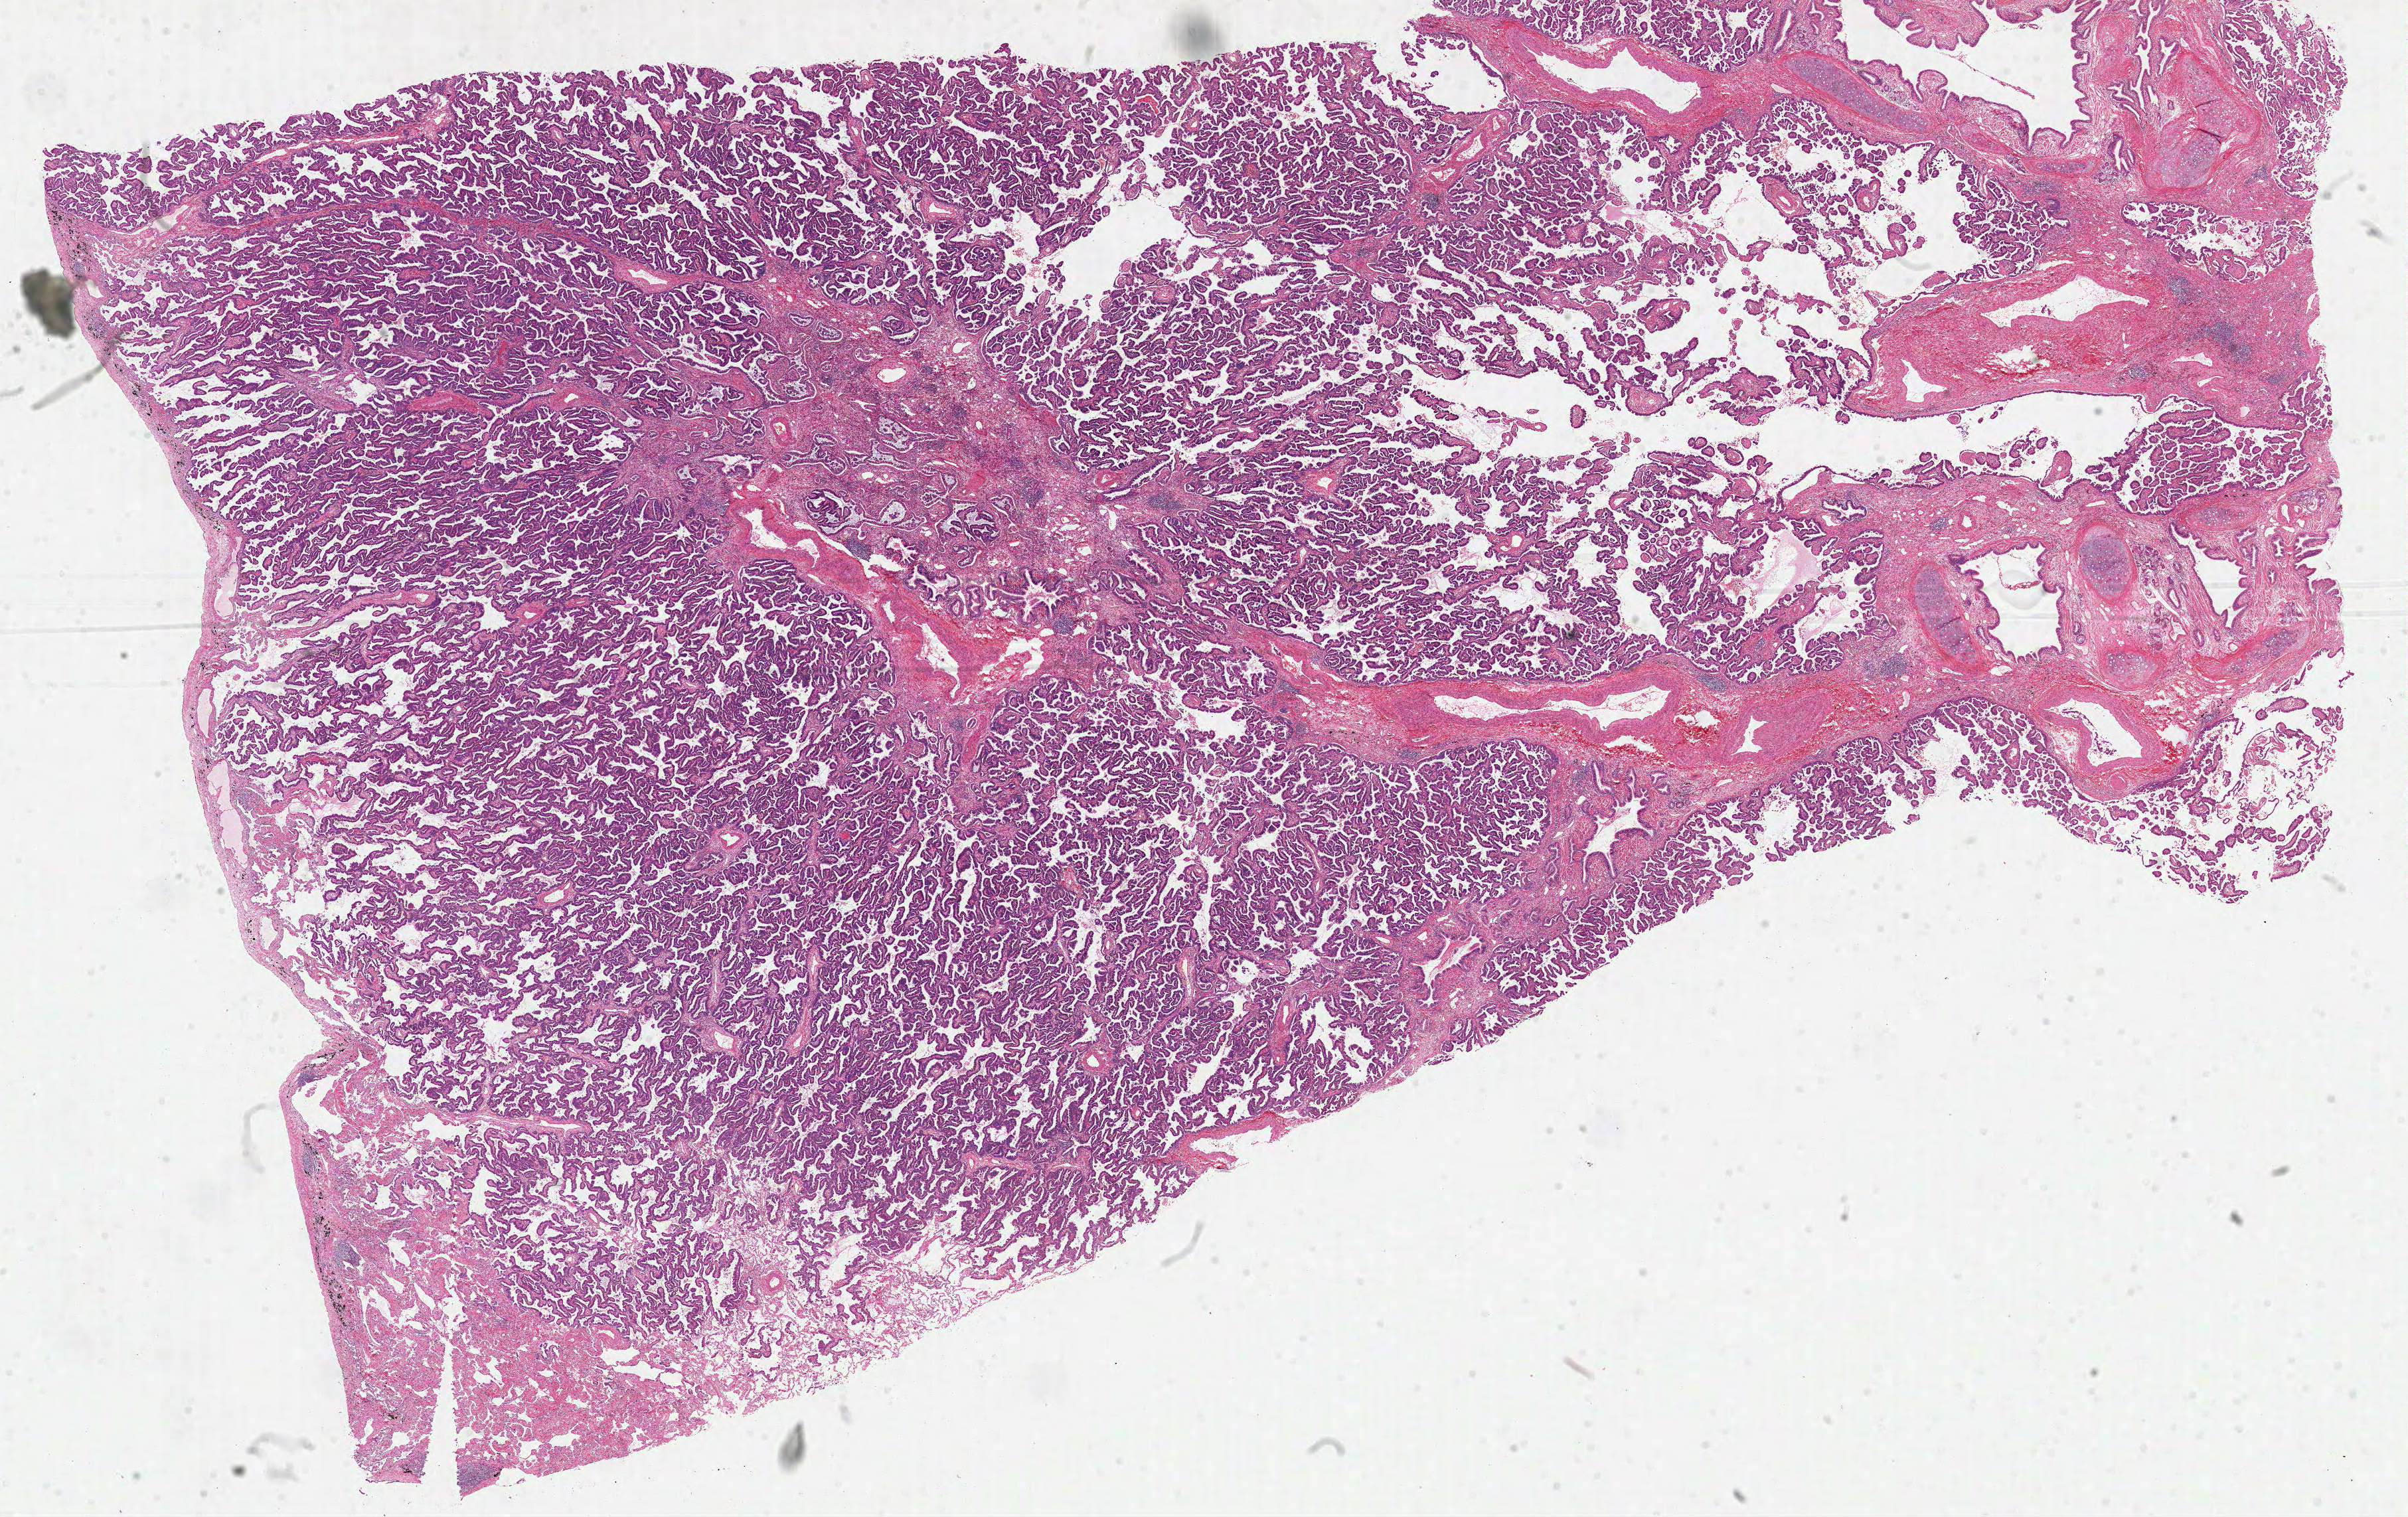
Digitized H&E-stained tissue section (whole slide), shown as a low-resolution overview of the whole scanned area (about 29.2 x 18.4 mm, from a 40x scan). FFPE section. Sample: primary tumour, lung. Male patient; age at initial diagnosis 77 years.
* AJCC pathologic stage: IV (6th edition)
* pathologic diagnosis: Papillary adenocarcinoma, NOS